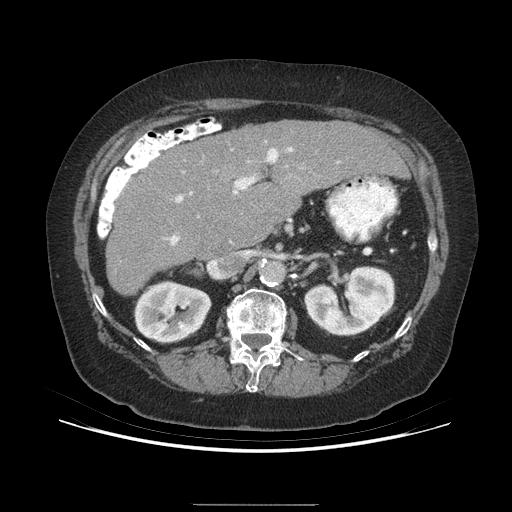
Contrast-enhanced abdominal CT (liver protocol), one axial slice; position 151 of 192 along the scan axis; reconstruction kernel STANDARD; soft-tissue window (W 400 / L 40 HU); 2.5 mm slice thickness; 512 × 512 image matrix, field of view 400 × 400 mm. From the clinical record (not read from this slice): diagnosis: hepatocellular carcinoma (patient treated with transarterial chemoembolisation; whether this scan precedes or follows treatment is not stated here); TNM stage (as recorded): Stage-I; Child-Pugh class: A; tumour nodularity: uninodular; tumour size: 3.2 cm.
Structures marked on this image (semi-automatically segmented with operator editing):
- liver parenchyma outside the tumour (the mass and vessels are separate outlines, so this box may not span the whole liver): bounding box <106,120,406,294> (left, top, right, bottom; pixels)
- liver vessels: <169,147,293,246>